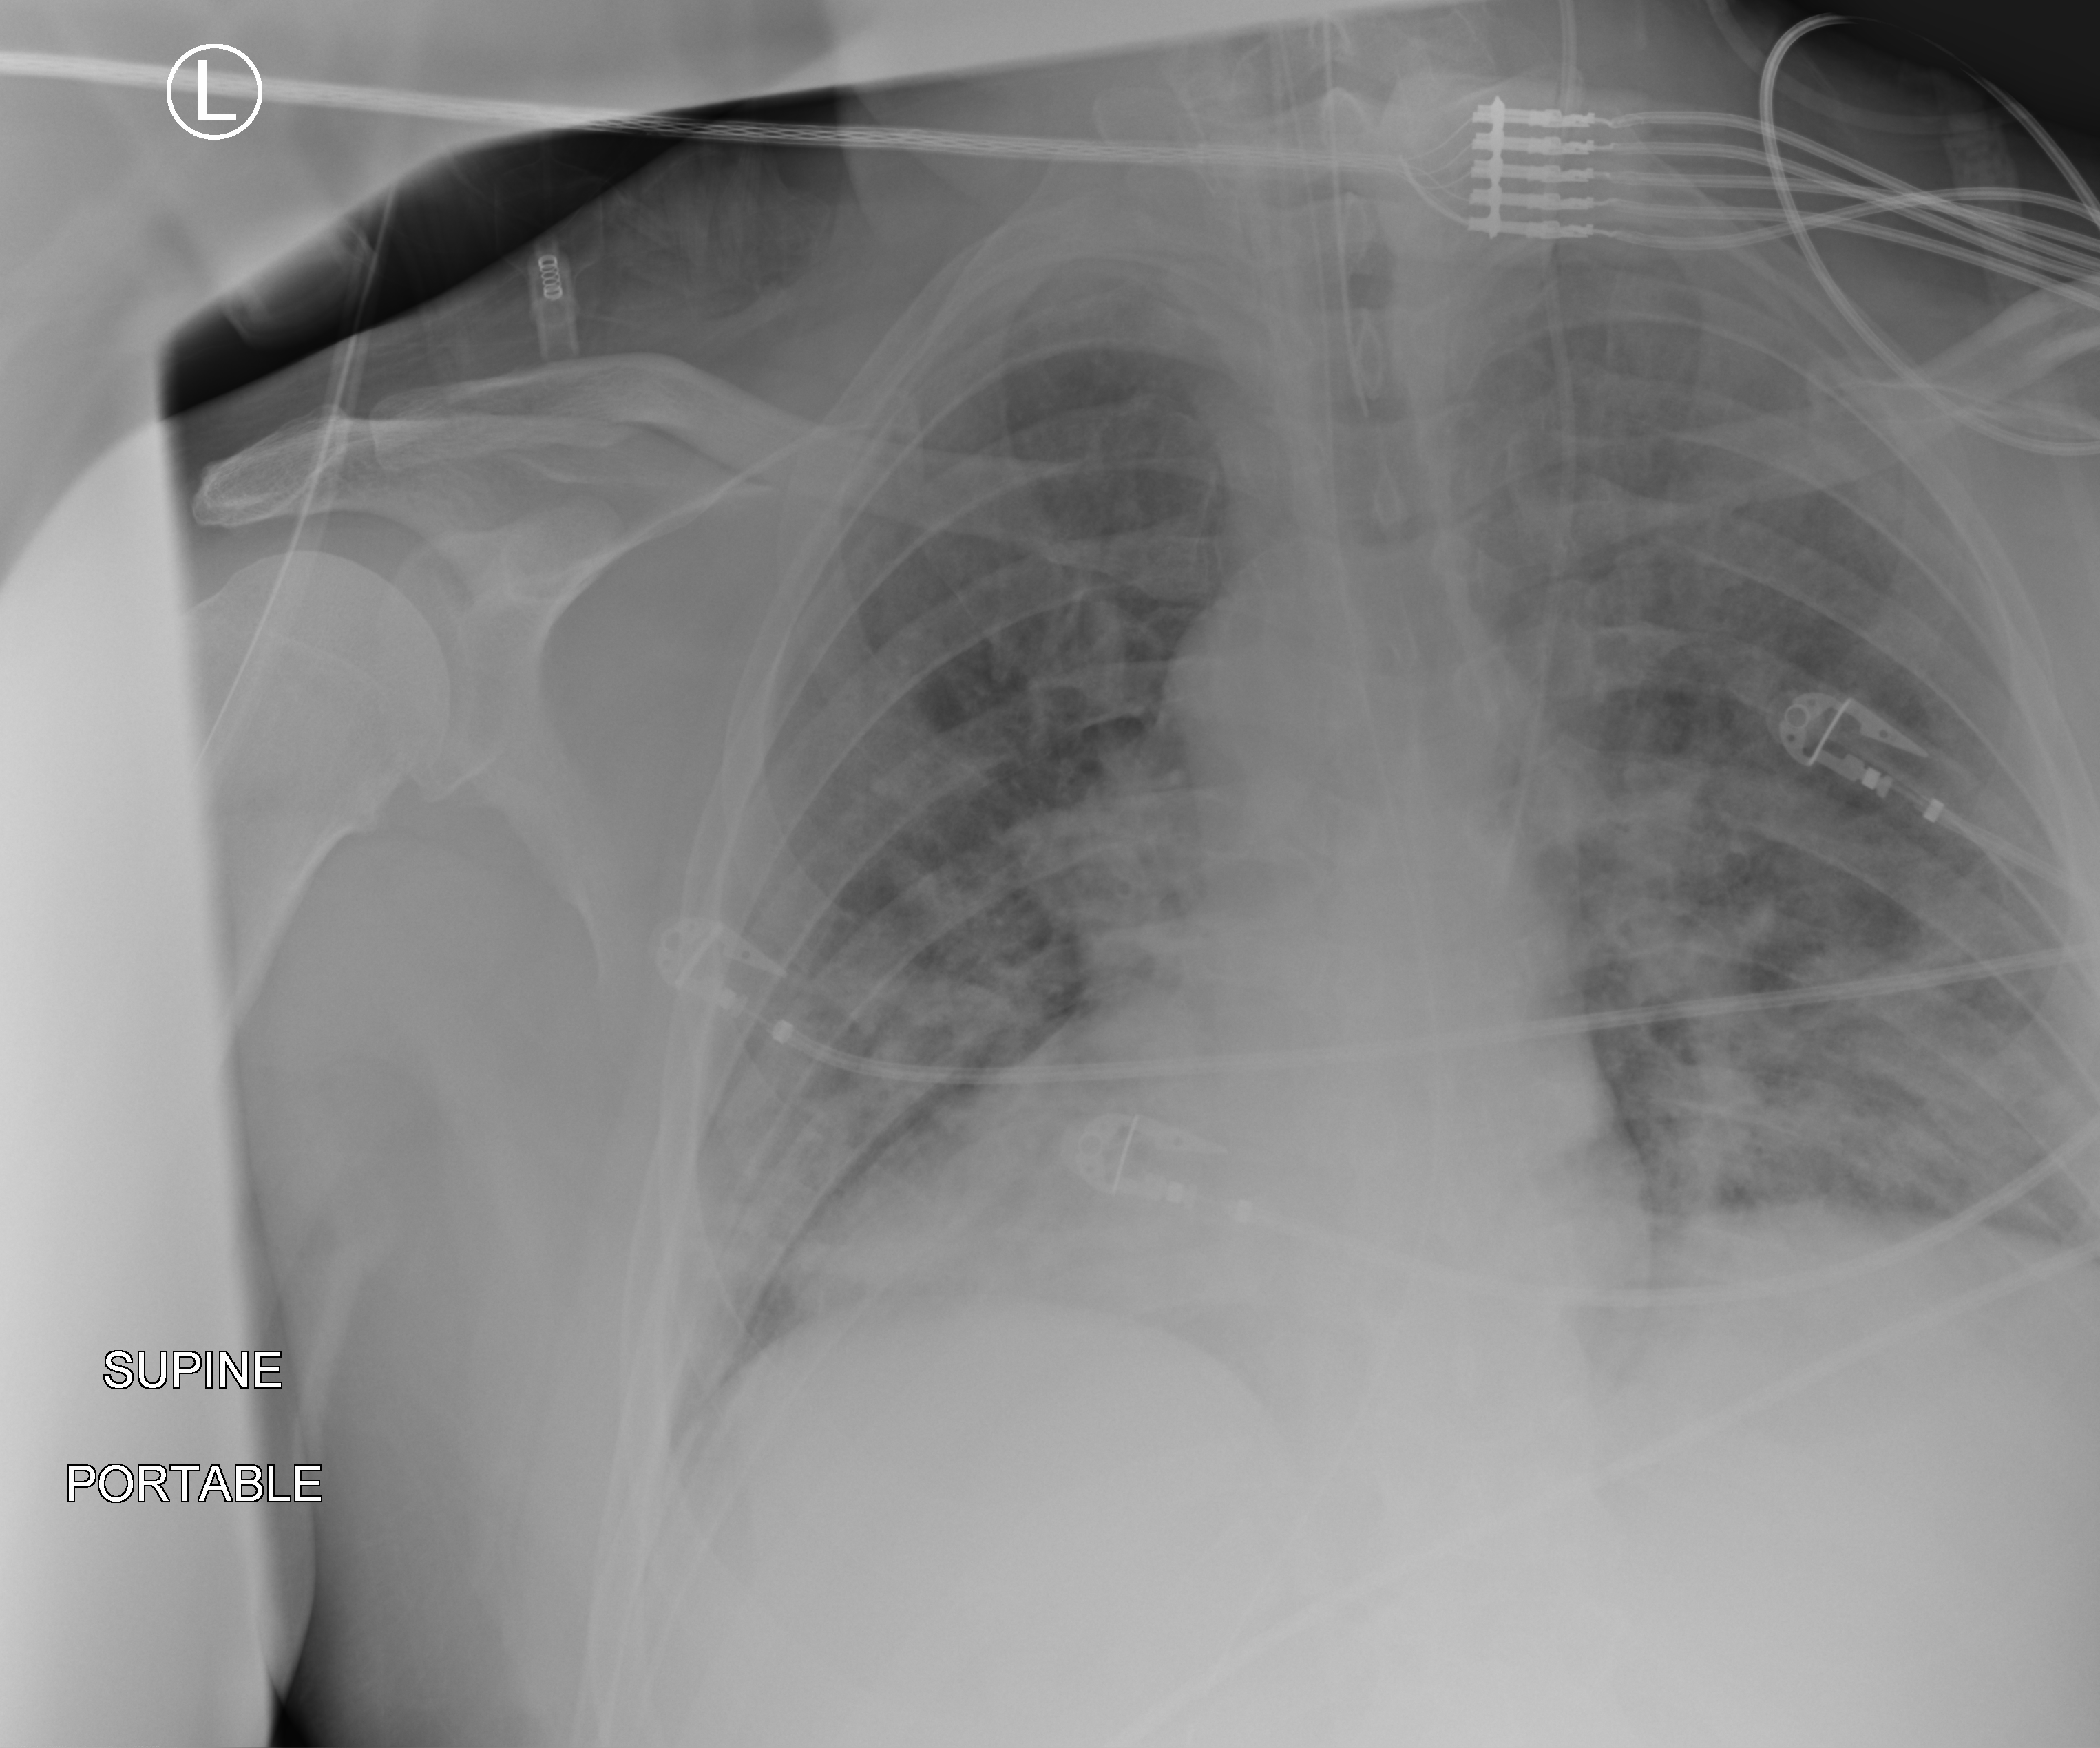
Chest X-ray (portable), posteroanterior (PA) projection. Male patient hospitalised with COVID-19, age 18–59 years.
Hospital-stay facts (about this admission, not read from this image; timing relative to this image not recorded):
- mechanically ventilated during this hospital stay: yes